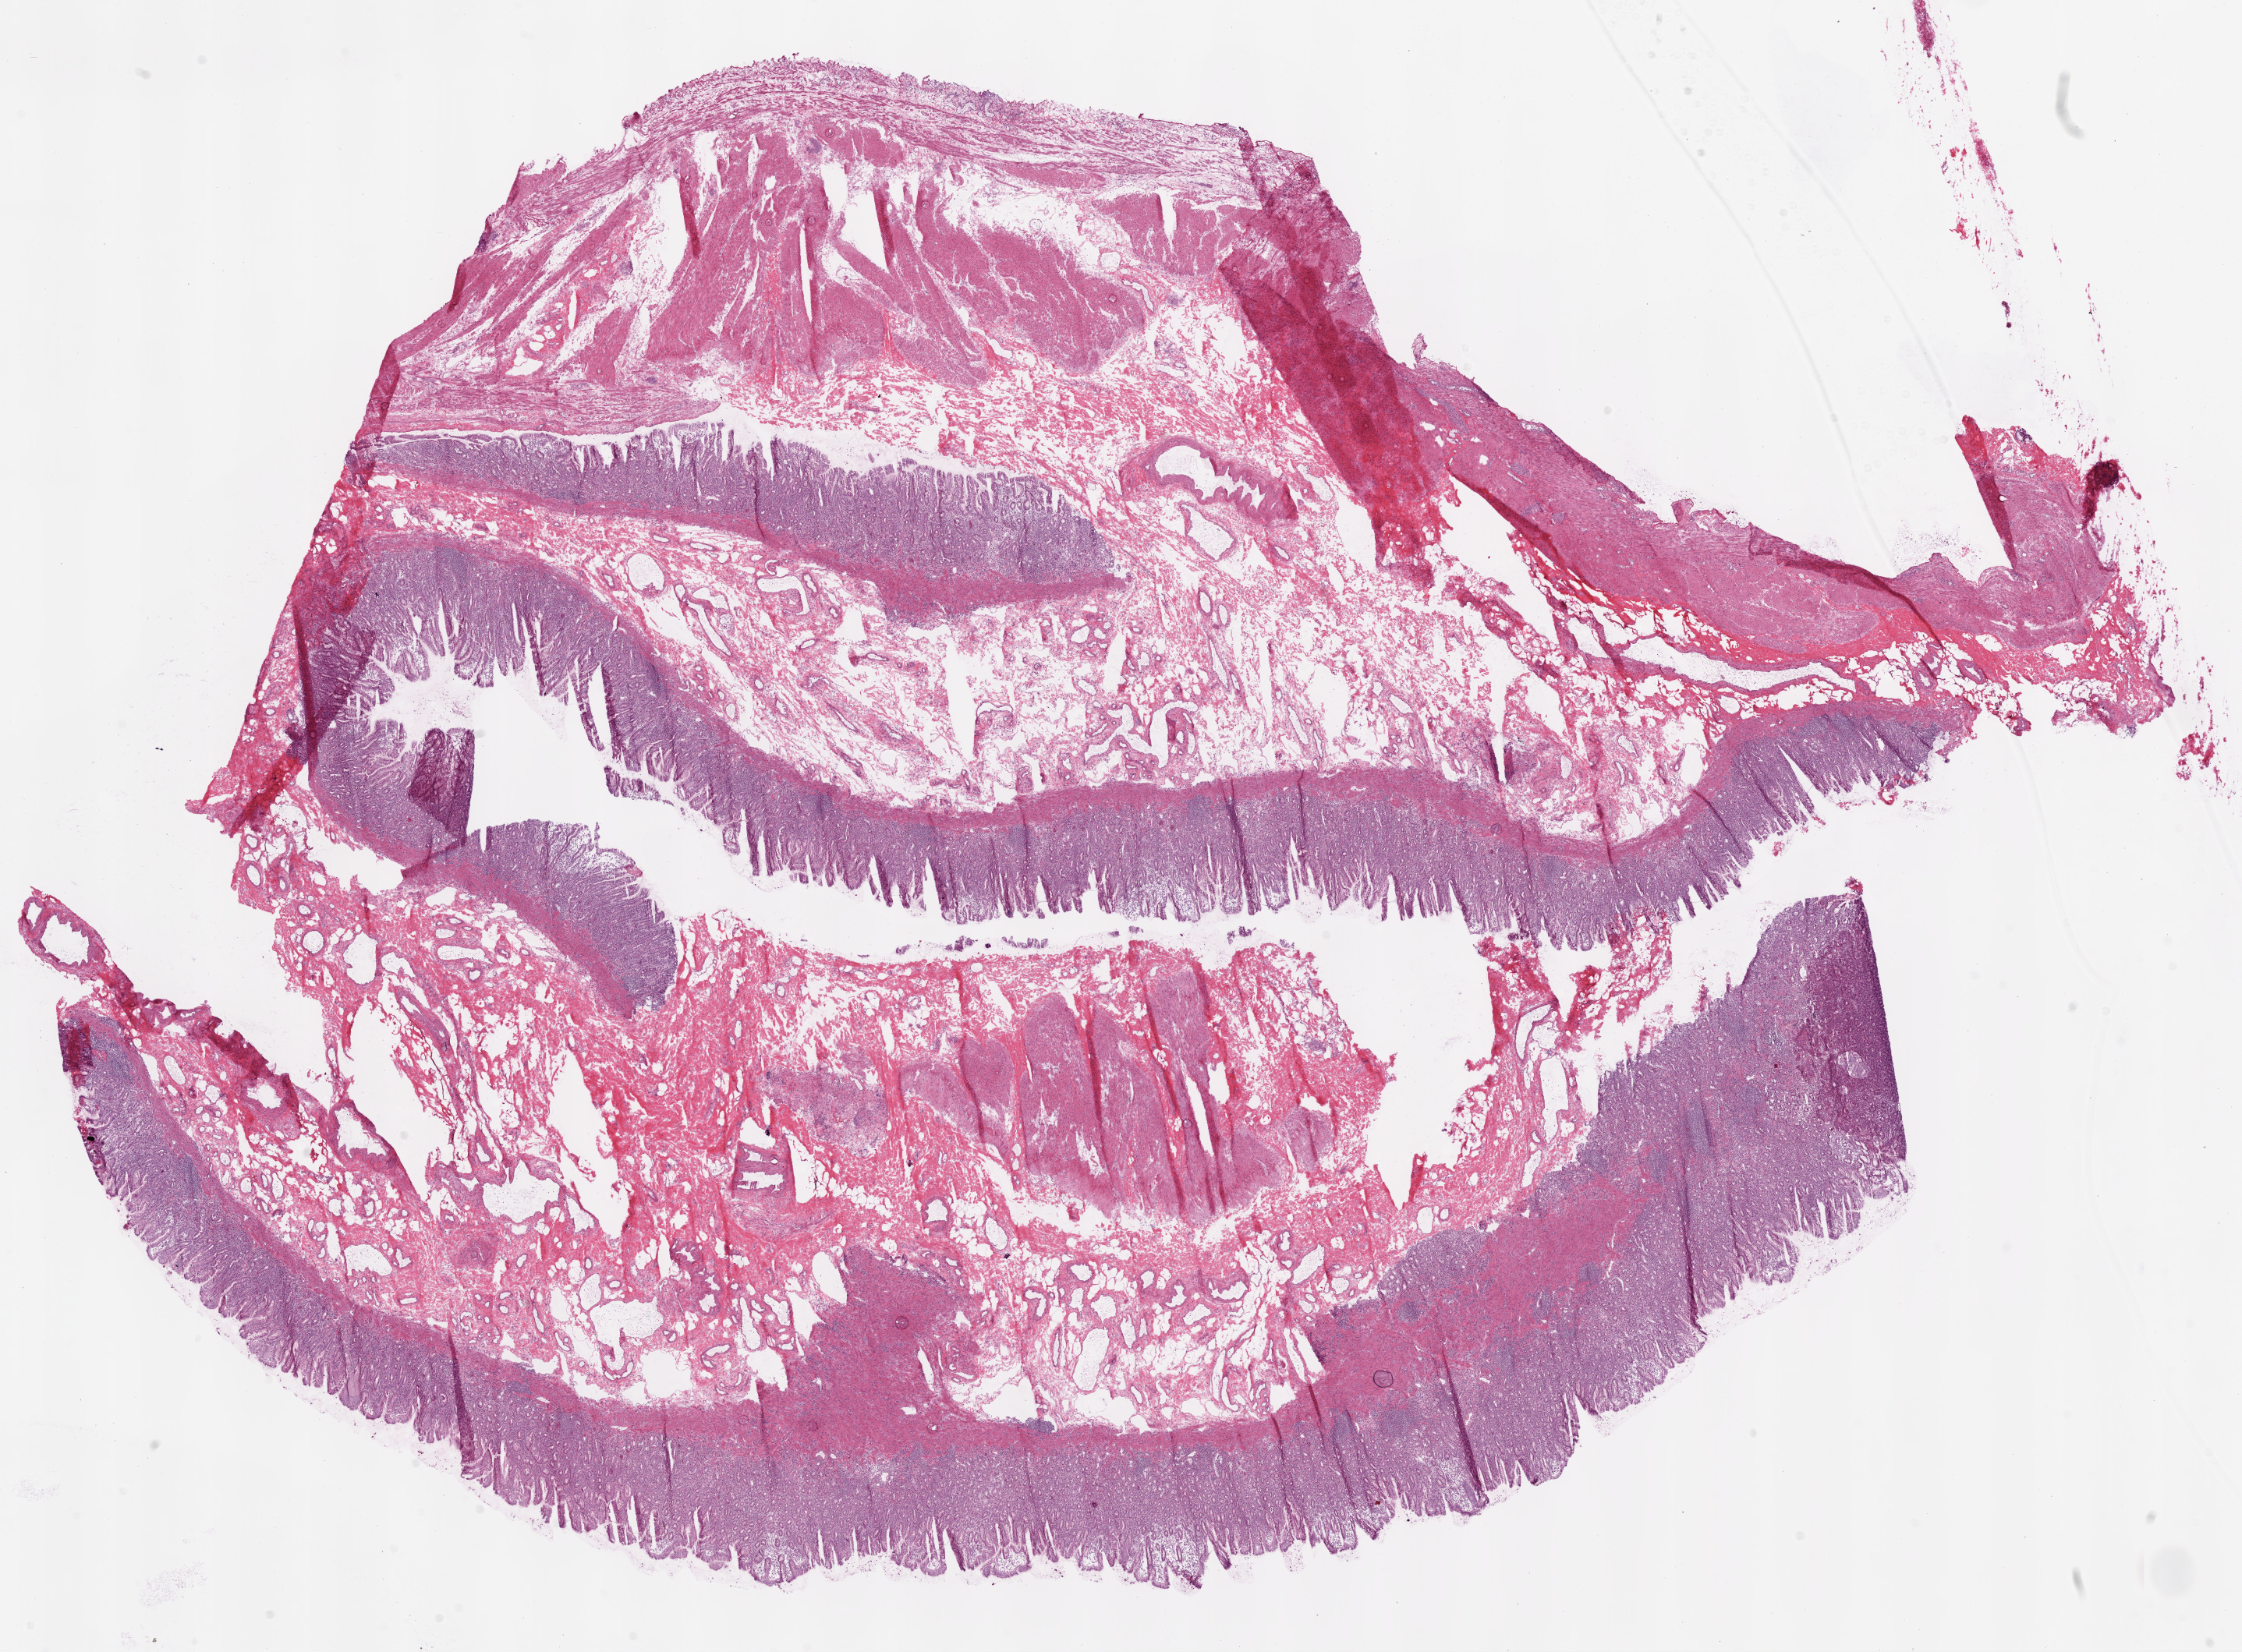
H&E-stained whole-slide image, low-resolution overview of the scanned area, about 23.1 x 17.0 mm (acquisition: 20x scan); frozen section from the bottom of the tissue portion; sample: solid tissue normal (non-tumour tissue), stomach. Female patient; age at initial diagnosis 79 years.
• this section: solid tissue normal (non-tumour) sample from the same patient
• patient diagnosis: Adenocarcinoma, NOS (gastric antrum)